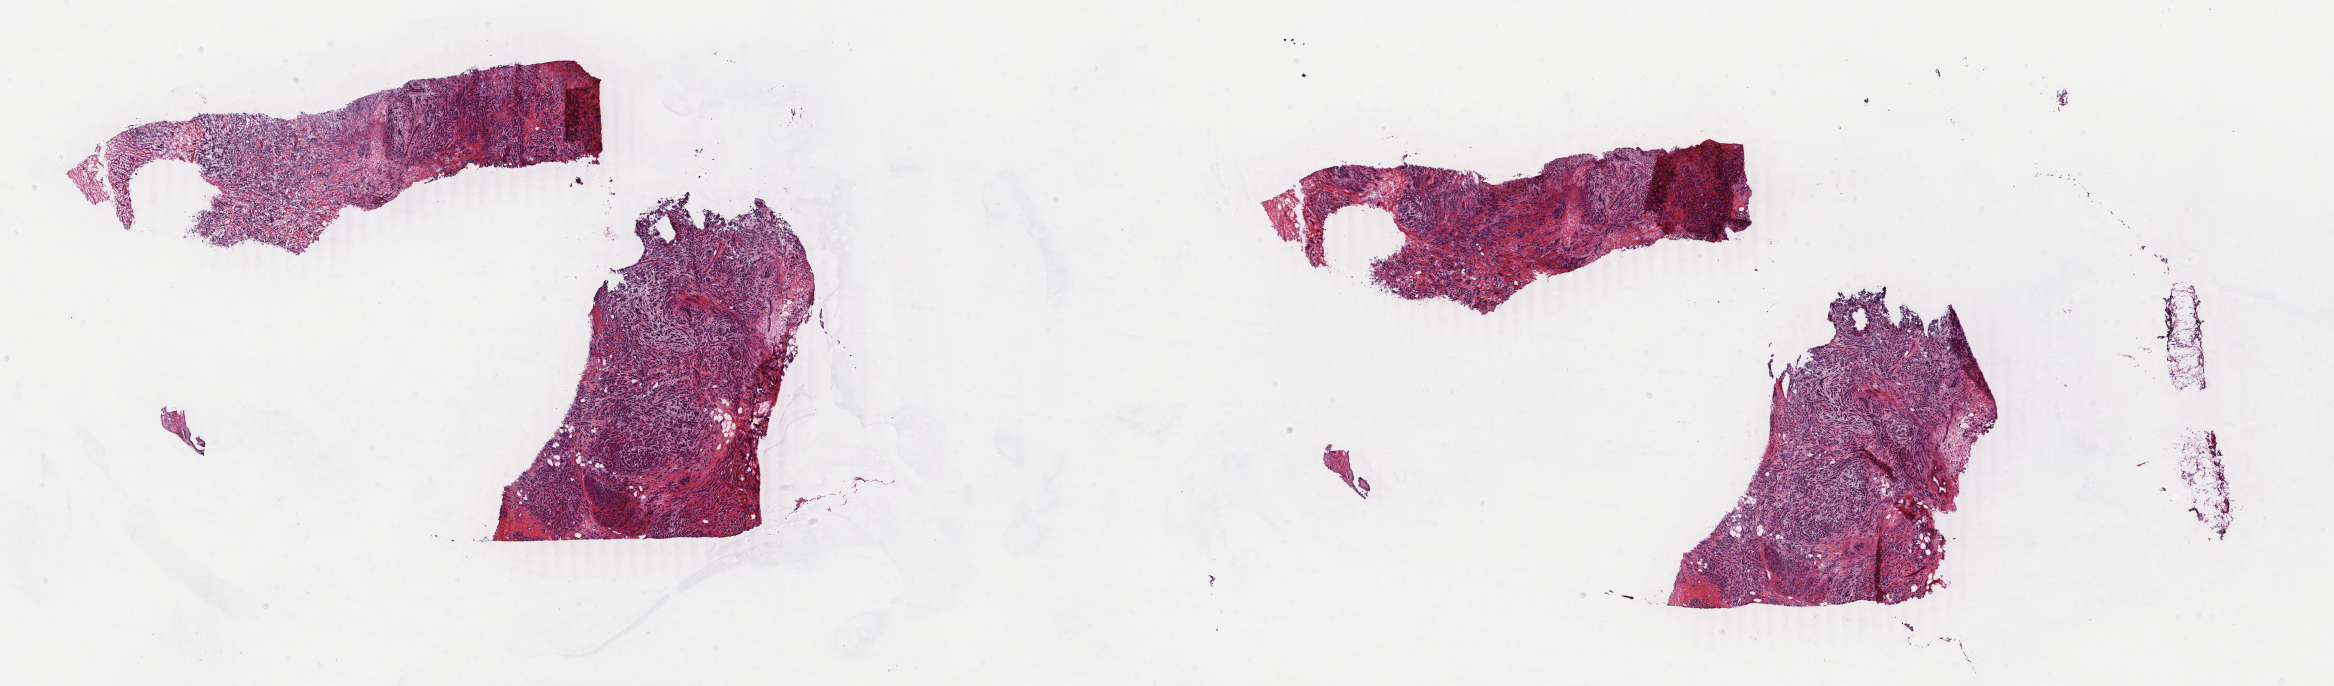
H&E whole-slide image — low-resolution overview of the scanned area, about 37.1 x 10.9 mm (slide scanned at 40x); frozen section; primary tumour sample from the breast. Patient: female, age at initial diagnosis 36 years. Slide review estimates, as recorded: tumour cells 80%, tumour nuclei 80%, normal cells 5%, stromal cells 15%, necrosis 0%. Inflammatory infiltration, as recorded: lymphocyte infiltration 1%, monocyte infiltration 0%, neutrophil infiltration 0%.
- AJCC pathologic stage: IIIC
- diagnosis: Infiltrating duct carcinoma, NOS
- TNM: T2 N3 M0